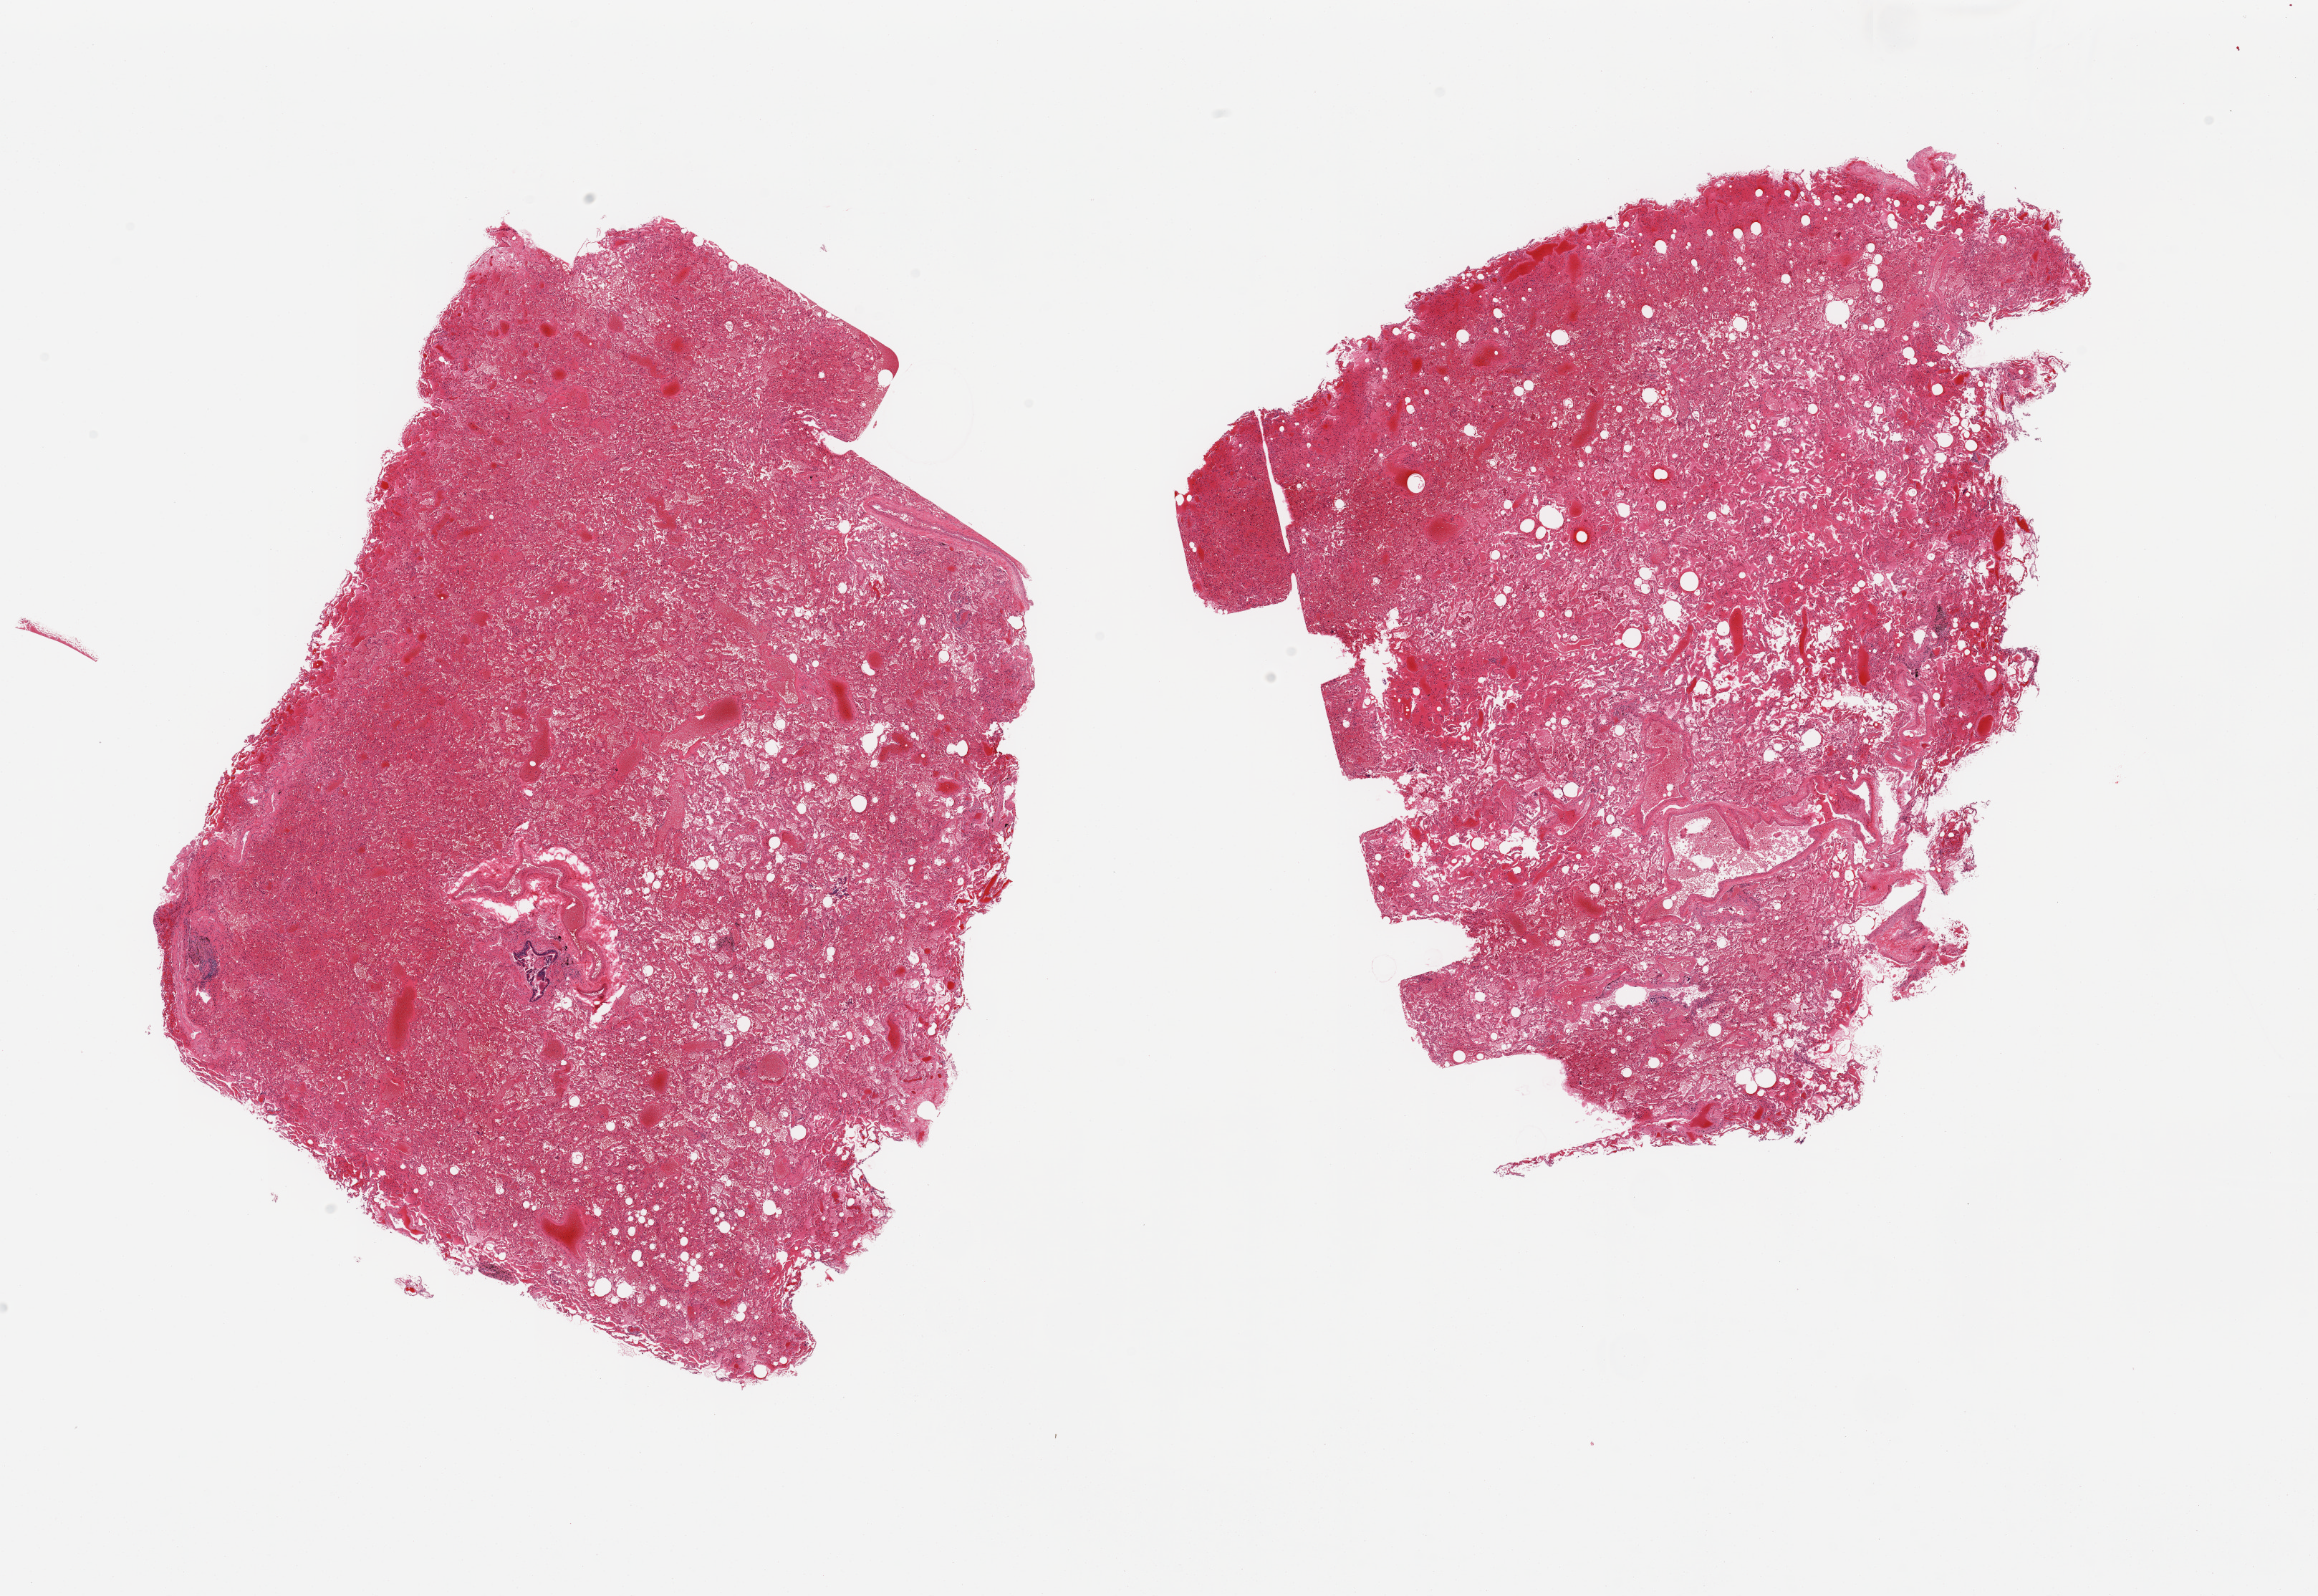
Digitized haematoxylin and eosin-stained section, brightfield, low-resolution overview of the scanned area, about 25.6 x 17.6 mm (slide scanned at 20x), PAXgene-fixed paraffin-embedded (PFPE) section, sampled site (target tissue): lung, tissue donor sample. Male donor.
Reviewer comment on this tissue sample: 2 pieces; moderate congestion and hemorrhage.